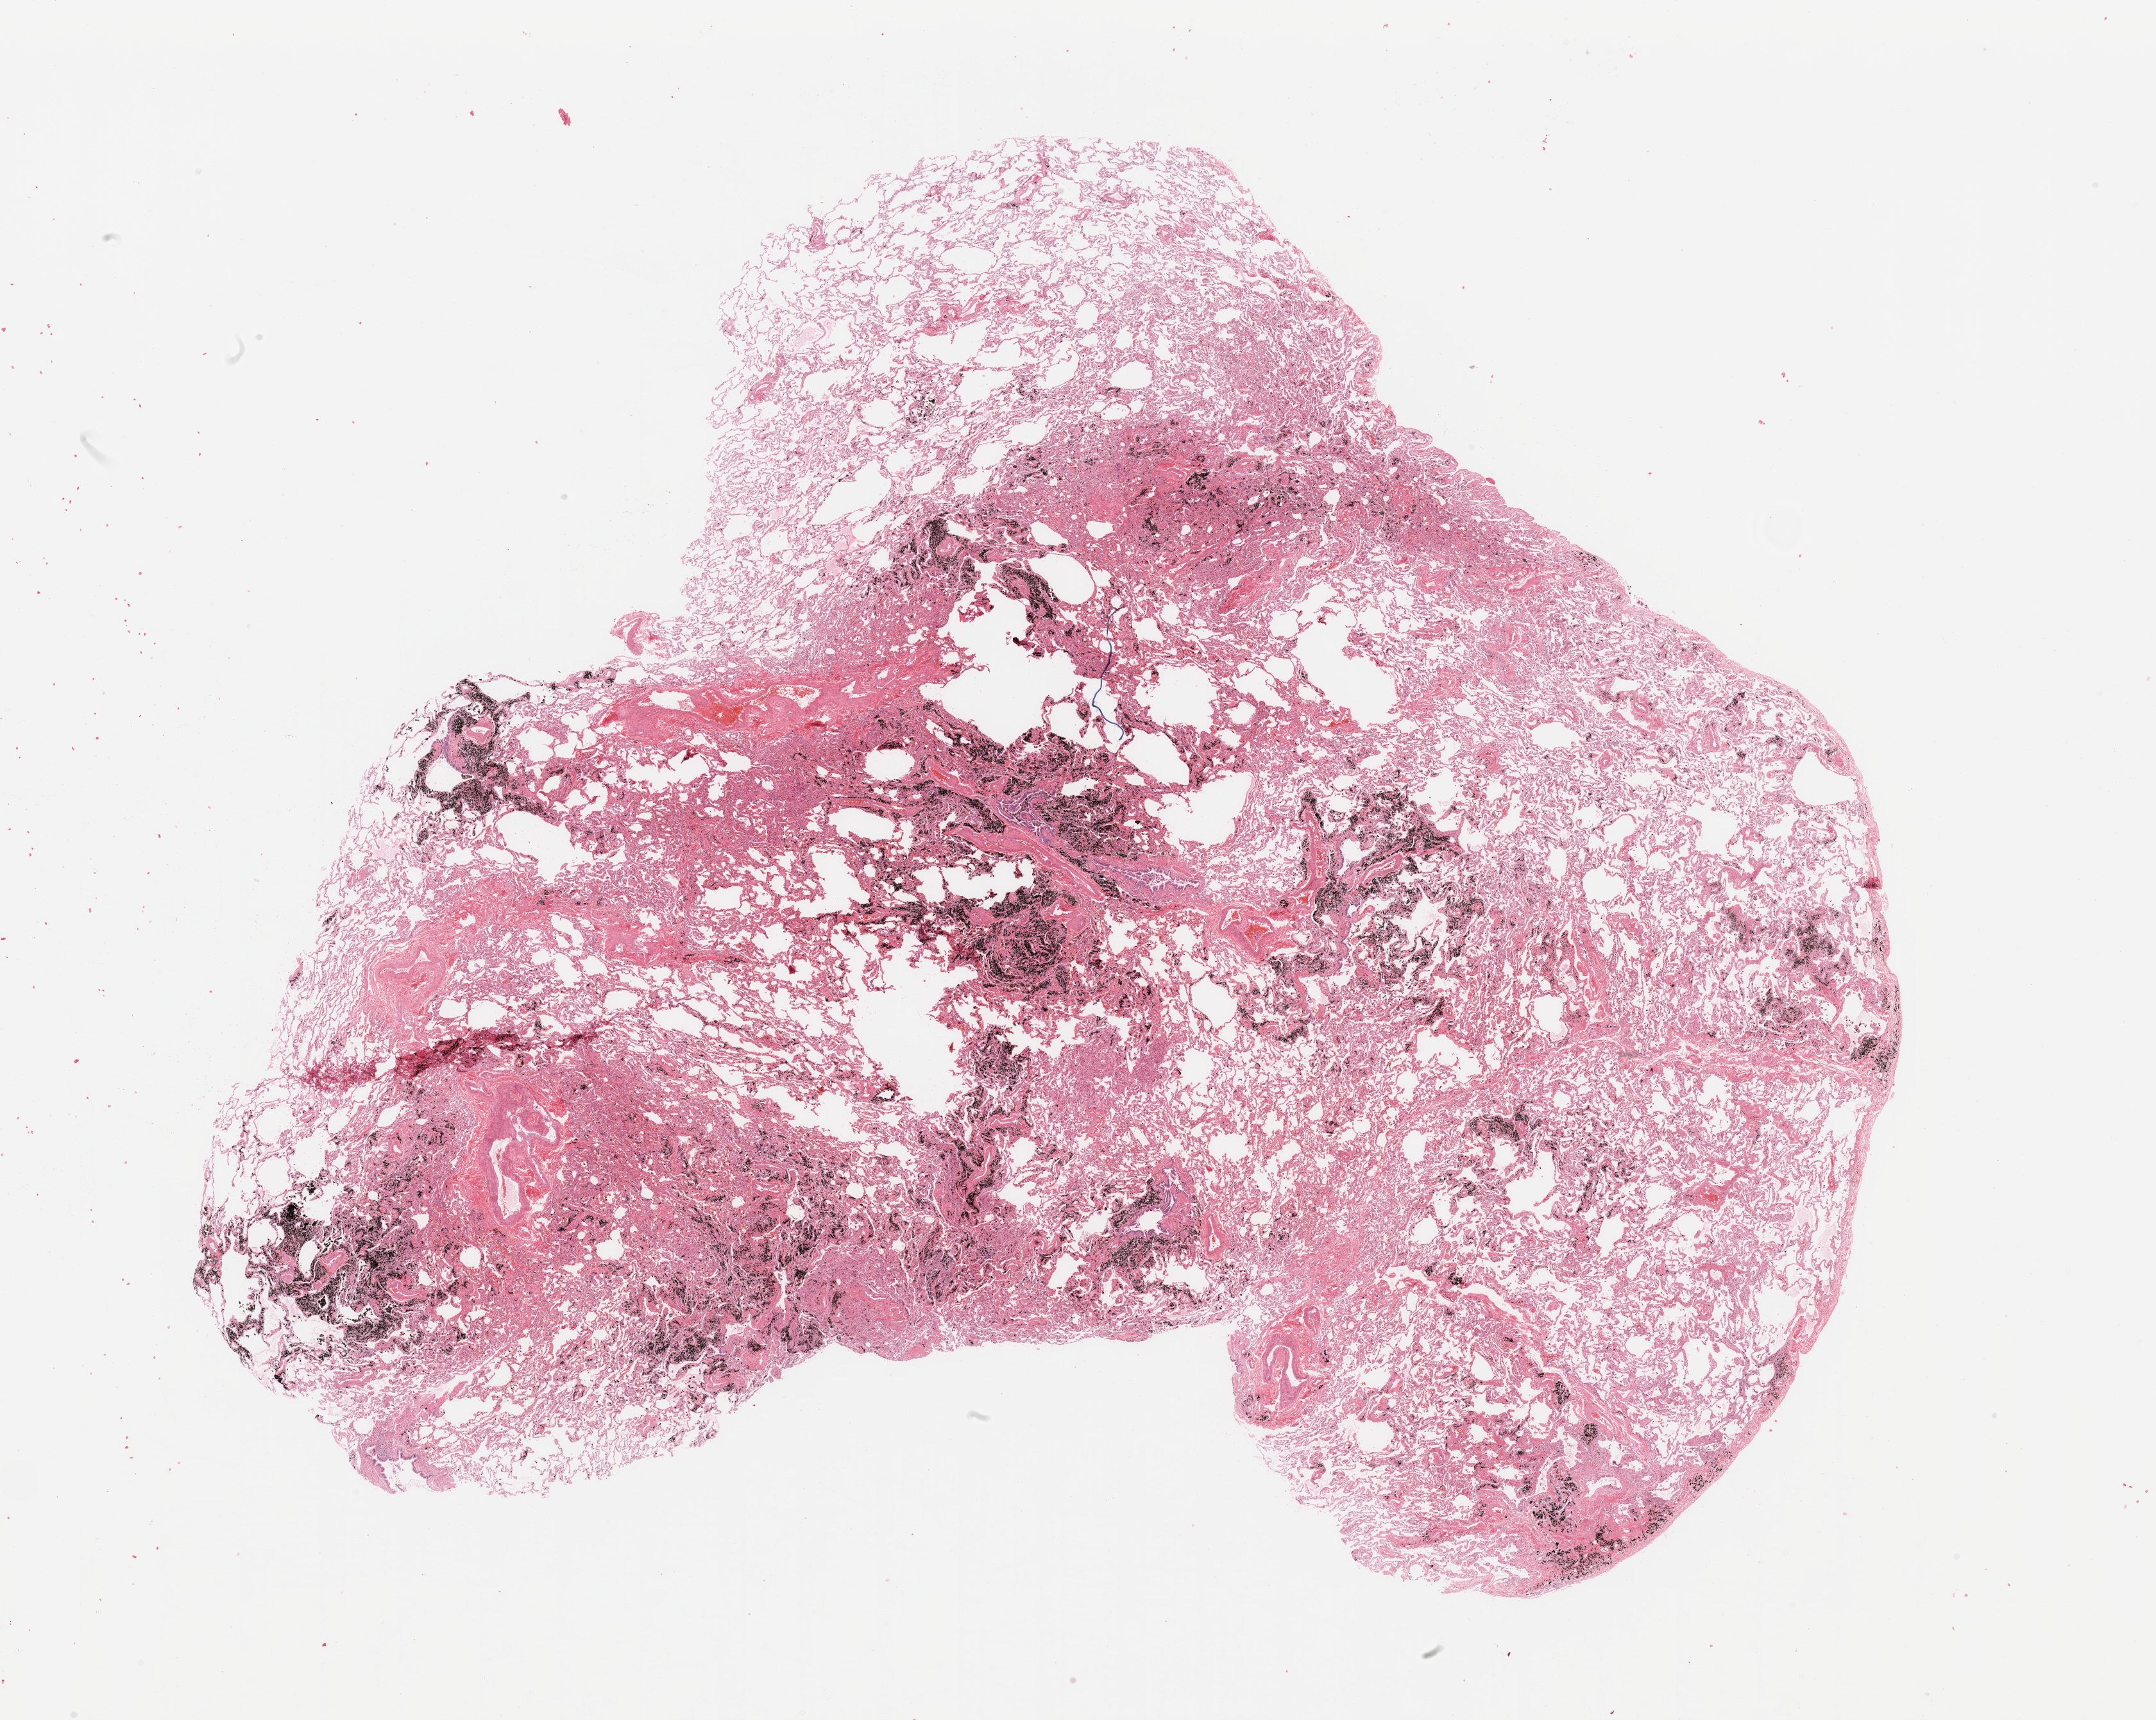
Digitized H&E tissue section (whole slide) — low-resolution overview of the scanned area, about 26.6 x 21.2 mm (acquisition: 20x scan). Normal (non-tumour) tissue sample, sampled site: lung. Patient: male, age 55 years.
This section: normal (non-tumour) tissue from the same patient. Patient diagnosis: Adenocarcinoma, NOS.